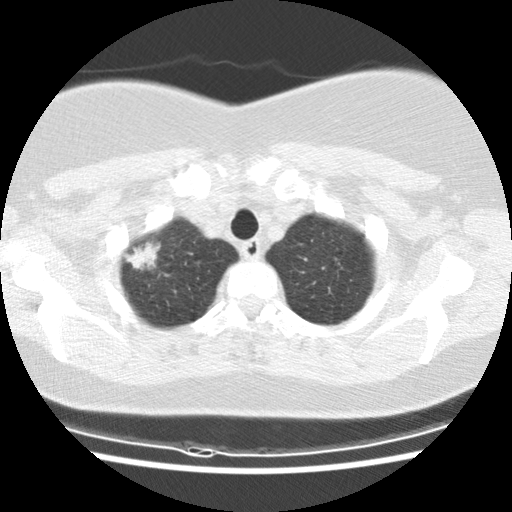
Axial slice from a low-dose chest CT screening exam. Baseline annual screen. Lung window (W 1500 / L -600 HU). 2.5 mm slice thickness. Standard (soft-tissue) reconstruction kernel (STANDARD). 512 × 512 image matrix. Female, age 61 years at enrolment. Former smoker at enrolment.
Expert-annotated lung lesion, bounding box (x1, y1, x2, y2) in pixels: (114, 230, 173, 285). Screening reader's record for this exam (one nodule recorded; not confirmed to be the boxed lesion): non-calcified nodule or mass ≥4 mm, right upper lobe, 26 × 16 mm, spiculated (stellate) margins, mixed attenuation. Official screen result: positive, change unspecified: nodule(s) >= 4 mm or enlarging nodule(s), mass(es), or other non-specific abnormalities suspicious for lung cancer. Participant outcome: lung cancer diagnosed 47 days after this screen — bronchiolo-alveolar carcinoma, mixed mucinous and non-mucinous, right upper lobe, well differentiated (G1), stage IA (AJCC 6th edition), 25 mm at pathology.